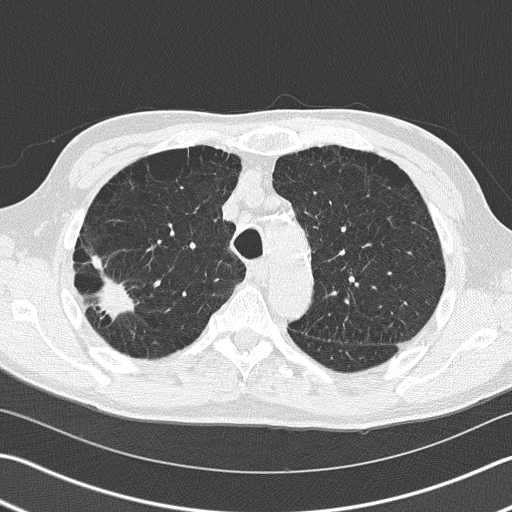
Low-dose screening chest CT, one axial slice; position 117 of 163 along the scan axis; reconstruction kernel B50f; lung window (W 1500 / L -600 HU); 512 × 512 image matrix, field of view 346 × 346 mm.
Annotated regions visible in this slice (expert manual segmentation):
- lesion 1 (tumor, upper lobe of right lung): box from (x=92, y=256) to (x=134, y=318) px